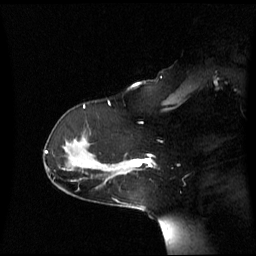
Breast MRI (dynamic contrast-enhanced), one sagittal slice; position 43 of 60 along the scan axis; dynamic contrast-enhanced series, image 2 of 3 at this slice position (ordered by acquisition); 1.5 T; TE 4.2 ms, TR 8.4 ms; 2.6 mm slice thickness; 256 × 256 image matrix. Female patient, age 39 years. From the clinical record (not read from this slice): setting: breast cancer imaged before/during neoadjuvant chemotherapy; receptor status: triple-negative.
Structures marked on this image (semi-automatically segmented with operator editing):
- analysis volume of interest (the breast-tissue region the enhancement analysis was run in; not a lesion): bounding box <117,155,152,175> (left, top, right, bottom; pixels)
- tumour enhancement mask (voxels above the 70 % enhancement threshold inside the analysis volume of interest): <132,158,152,167>